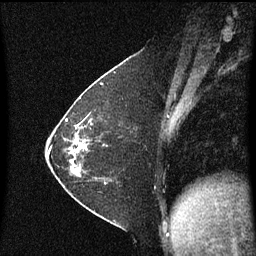
Breast MRI (dynamic contrast-enhanced), one sagittal slice. Slice 24 of 60 in the series (ordered by position). Dynamic contrast-enhanced series, image 2 of 3 at this slice position (ordered by acquisition). 1.5 T. TE 4.2 ms, TR 8.4 ms. 256 × 256 image matrix, field of view 200 × 200 mm. Female patient, age 36 years. Case-level facts recorded for this patient, not image findings: setting: breast cancer imaged before/during neoadjuvant chemotherapy; receptor status: HR-positive, HER2-negative.
Outlined on this slice (semi-automatically segmented with operator editing):
- analysis volume of interest (the breast-tissue region the enhancement analysis was run in; not a lesion): bounding box (x1, y1, x2, y2) in pixels: (72, 116, 107, 185)
- tumour enhancement mask (voxels above the 70 % enhancement threshold inside the analysis volume of interest): (72, 126, 85, 171)